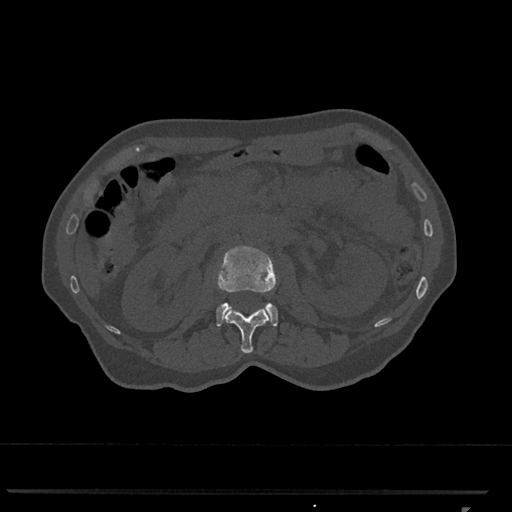
CT including the spine, one axial slice. Position 373 of 793 along the scan axis. 120 kVp. Bone window (W 1800 / L 400 HU). 0.5 mm slice thickness. 512 × 512 image matrix, field of view 380 × 380 mm. Female patient, age 62 years. Case-level facts recorded for this patient, not image findings: primary cancer: renal.
Annotated regions visible in this slice (semi-automatically segmented with operator editing):
- L1 vertebra: bounding box (x1, y1, x2, y2) in pixels: (224, 307, 270, 353)
- L2 vertebra: (216, 246, 278, 327)